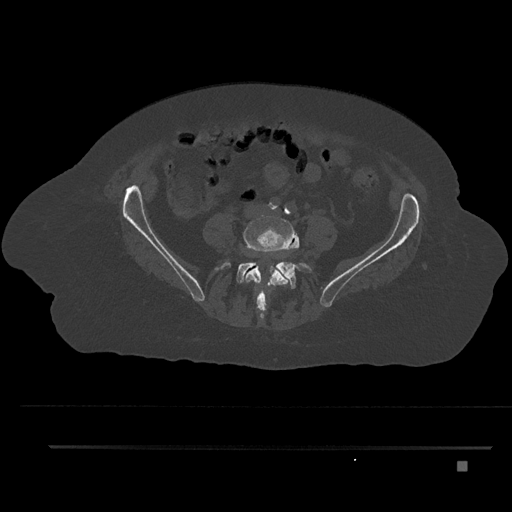
CT including the spine, one axial slice; slice 59 of 797 in the series (ordered by position); reconstruction kernel Br40s/3; 120 kVp; bone window (W 1800 / L 400 HU); 0.5 mm slice thickness; 512 × 512 image matrix. Patient: female, 76 years. From the clinical record (not read from this slice): primary cancer: lung; vertebrae with lytic lesions (as recorded): T11, L3.
Structures marked on this image (semi-automatic segmentation, software-assisted and operator-edited):
- L4 vertebra: box from (x=244, y=216) to (x=298, y=315) px
- L5 vertebra: (x=215, y=248)–(x=312, y=318)